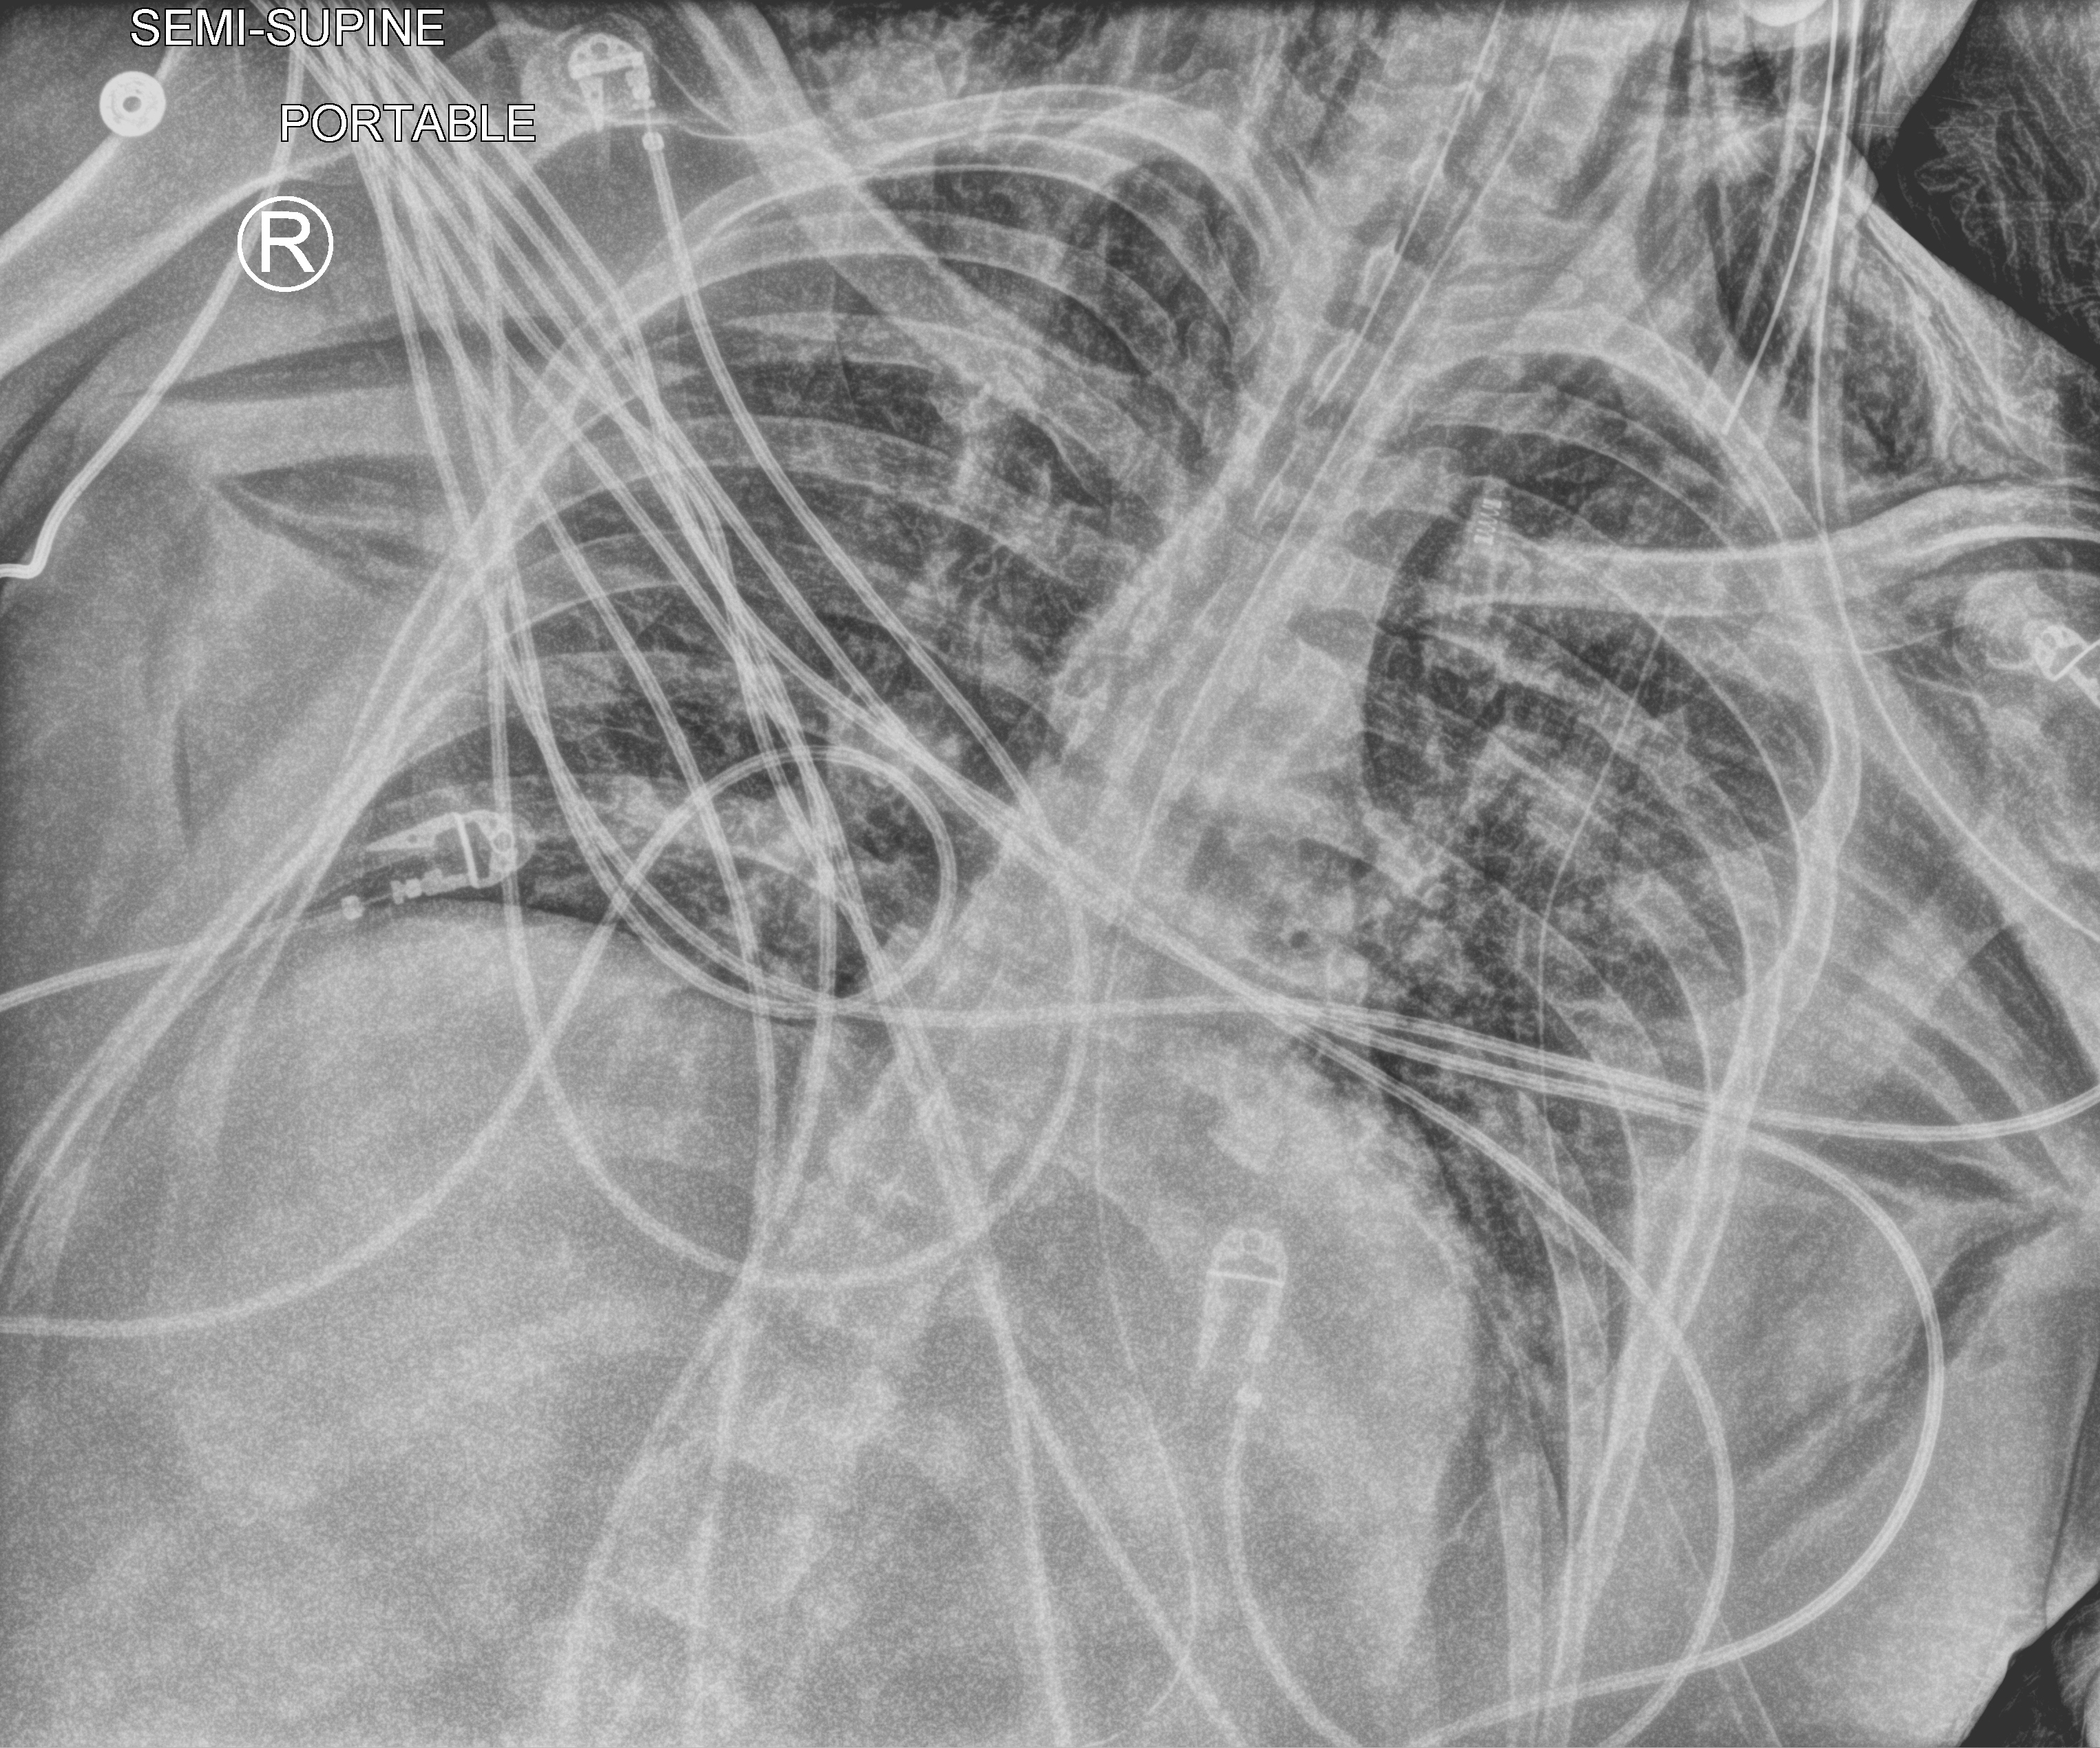
Bedside chest radiograph (computed radiography); anteroposterior (AP) projection. Patient hospitalised with COVID-19; male, aged 18–59 years.
Admission-level facts for this patient (not findings on this image; timing relative to this image not recorded):
- admitted to intensive care during this hospital stay: yes
- mechanically ventilated during this hospital stay: yes